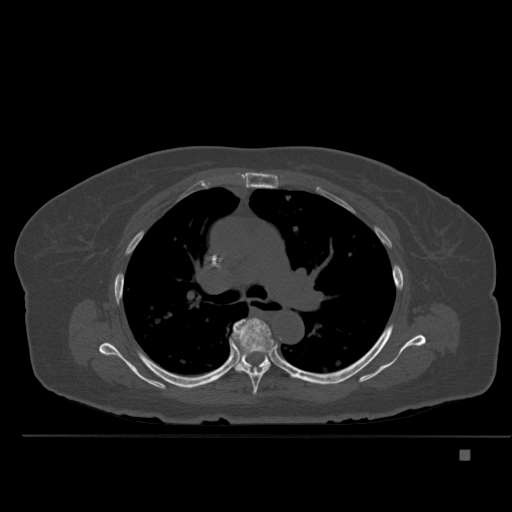
CT including the spine, one axial slice; slice 348 of 477 in the series (ordered by position); bone window (W 1800 / L 400 HU); 1.5 mm slice thickness; 512 × 512 image matrix, field of view 422 × 422 mm. Patient: female, 74 years. Case-level facts recorded for this patient, not image findings: primary cancer: colon.
Outlined on this slice (semi-automatic segmentation, software-assisted and operator-edited):
- T5 vertebra: bounding box (x1, y1, x2, y2) in pixels: (233, 318, 275, 395)
- T6 vertebra: (229, 321, 270, 370)